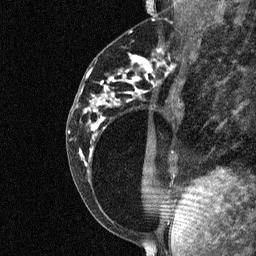
Breast MRI (dynamic contrast-enhanced), one sagittal slice; position 28 of 64 along the scan axis; dynamic contrast-enhanced study with each time point stored as its own series, time point 2 of 3 at this slice position (early post-contrast, ordered by acquisition time); 1.5 T; TE 4.8 ms, TR 27 ms; 2 mm slice thickness; 256 × 256 image matrix, field of view 180 × 180 mm. Female patient, age 34 years. Case-level facts recorded for this patient, not image findings: setting: breast cancer imaged before/during neoadjuvant chemotherapy; receptor status: HR-positive, HER2-negative.
Outlined on this slice (semi-automatically segmented with operator editing):
- analysis volume of interest (the breast-tissue region the enhancement analysis was run in; not a lesion): bounding box <78,44,181,191> (left, top, right, bottom; pixels)
- tumour enhancement mask (voxels above the 90 % enhancement threshold inside the analysis volume of interest): <100,50,161,104>